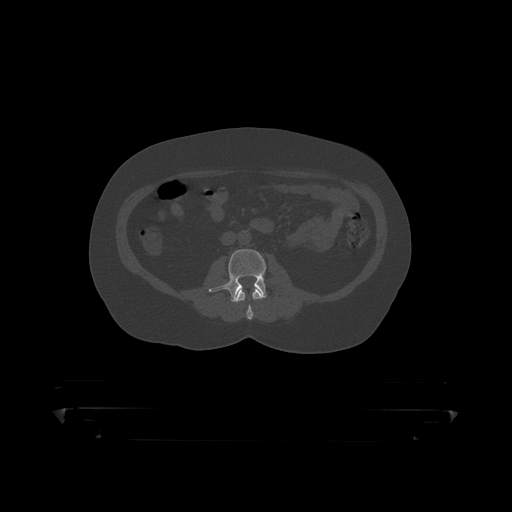
CT including the spine, one axial slice; slice 99 of 390 in the series (ordered by position); bone window (W 1800 / L 400 HU); 1.25 mm slice thickness; 512 × 512 image matrix, field of view 650 × 650 mm. Male patient, age 60 years. From the clinical record (not read from this slice): primary cancer: prostate.
Outlined on this slice (semi-automatic segmentation, software-assisted and operator-edited):
- L2 vertebra: bounding box [x1, y1, x2, y2] px = [235, 288, 264, 319]
- L3 vertebra: [209, 249, 267, 303]